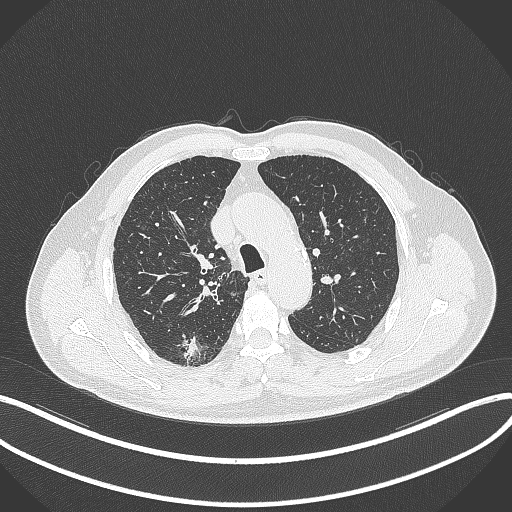
Chest CT, one axial slice; slice 270 of 359 in the series (ordered by position); reconstruction kernel B70f; 120 kVp; lung window (W 1500 / L -600 HU); 1 mm slice thickness; 512 × 512 image matrix, field of view 400 × 400 mm. Patient: male, 69 years. From the clinical record (not read from this slice): clinical TNM (as recorded): T1b N0 M0; histopathological grade: G2-3.
Structures marked on this image (rectangle marked by the reading radiologist):
- lung tumour (recorded histology: adenocarcinoma): bounding box <178,332,203,365> (left, top, right, bottom; pixels)